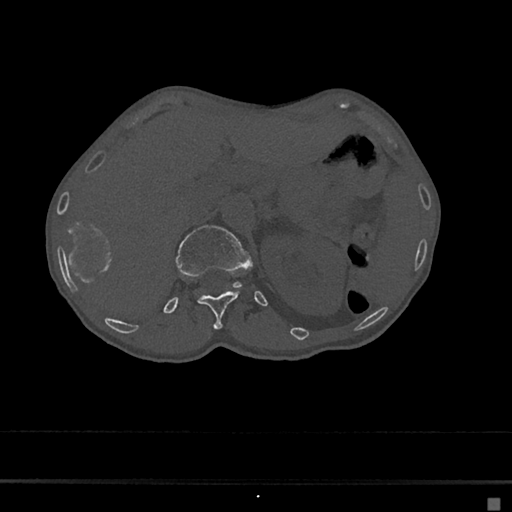
CT including the spine, one axial slice; slice 105 of 797 in the series (ordered by position); bone window (W 1800 / L 400 HU); 0.5 mm slice thickness; 512 × 512 image matrix, field of view 360 × 360 mm. Female patient, age 68 years. Case-level facts recorded for this patient, not image findings: primary cancer: renal.
Outlined on this slice (semi-automatic segmentation, software-assisted and operator-edited):
- L1 vertebra: box from (x=175, y=225) to (x=251, y=287) px
- T12 vertebra: (x=198, y=291)–(x=238, y=329)